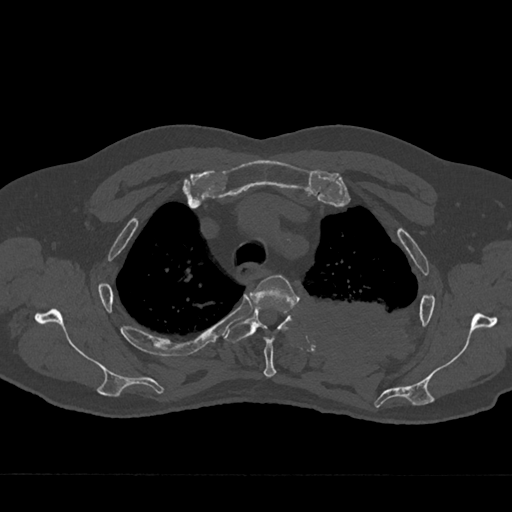
CT including the spine, one axial slice; slice 543 of 797 in the series (ordered by position); reconstruction kernel Br40s/3; 120 kVp; bone window (W 1800 / L 400 HU); 0.5 mm slice thickness; 512 × 512 image matrix, field of view 377 × 377 mm. Male patient, age 75 years. From the clinical record (not read from this slice): primary cancer: renal.
Annotated regions visible in this slice (semi-automatic segmentation, software-assisted and operator-edited):
- T3 vertebra: bounding box (x1, y1, x2, y2) in pixels: (250, 275, 298, 377)
- T4 vertebra: (224, 306, 292, 344)